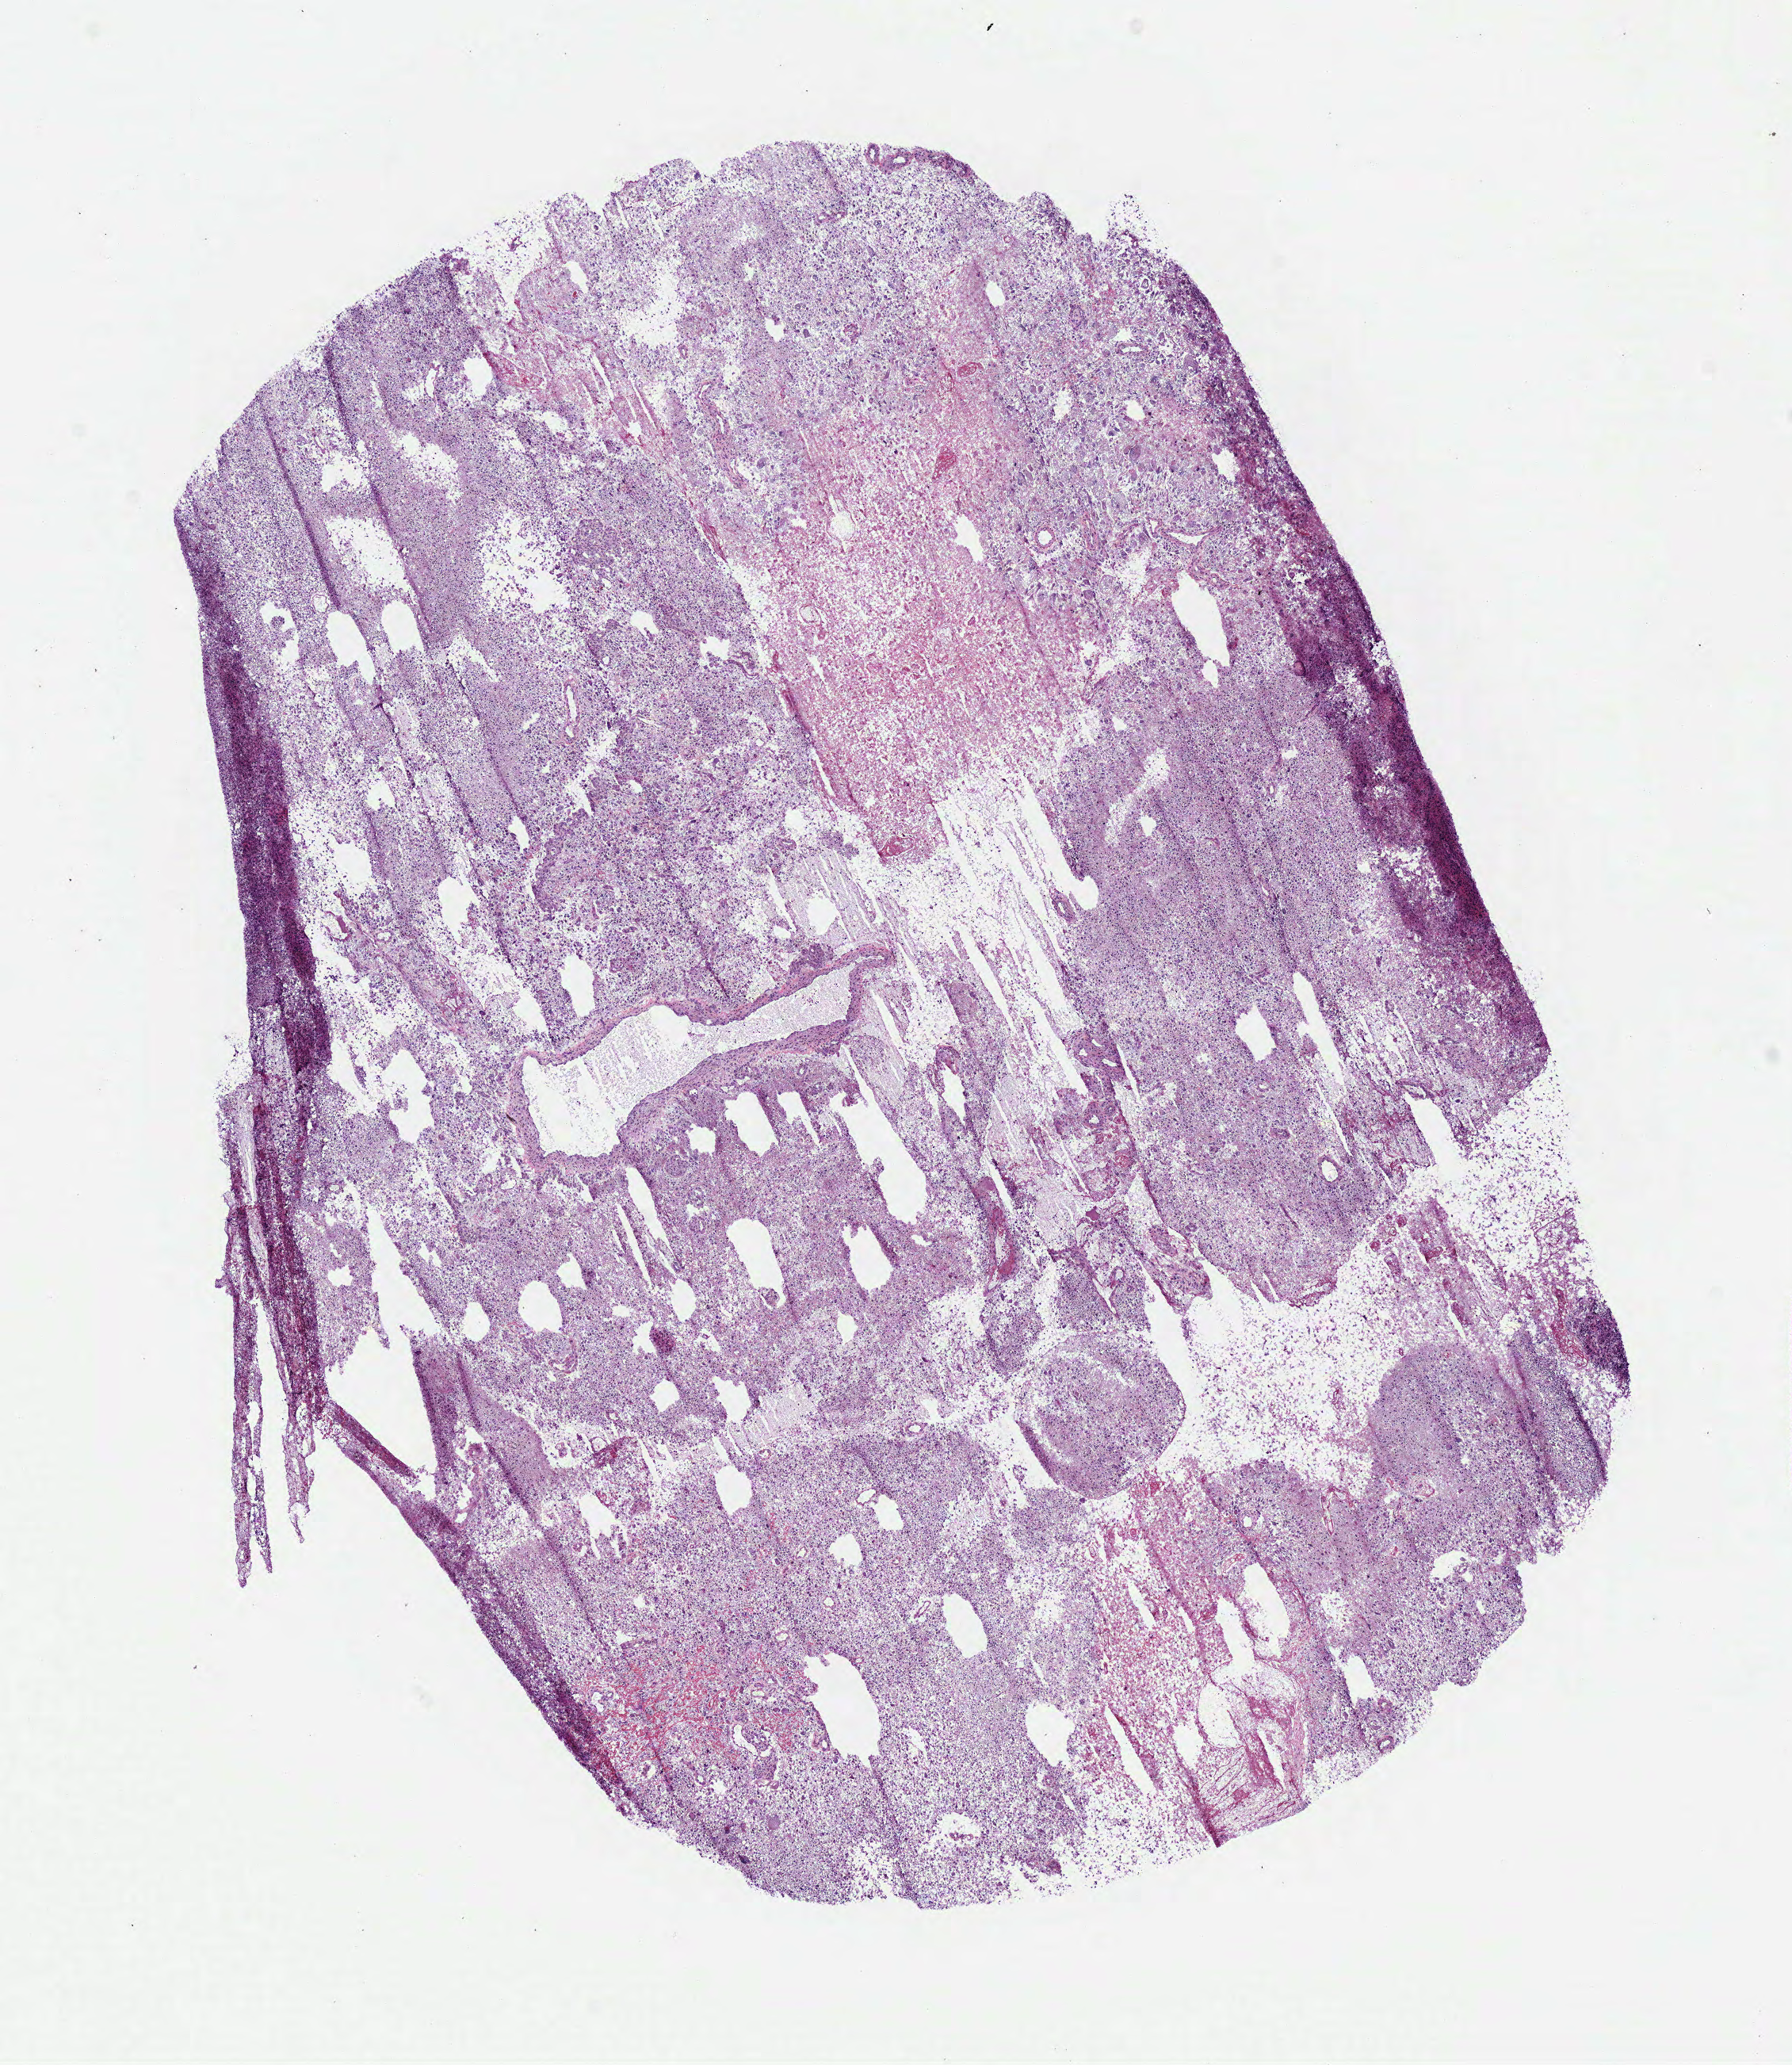
Digitized H&E tissue section (whole slide), whole scanned area (about 8.9 x 10.3 mm) shown as a low-resolution overview; frozen section from the bottom of the tissue portion; sample: primary tumour, brain. Female, age 45 years at initial diagnosis. Slide review estimates, as recorded: tumour cells 85%, tumour nuclei 80%.
Diagnosis: Glioblastoma.